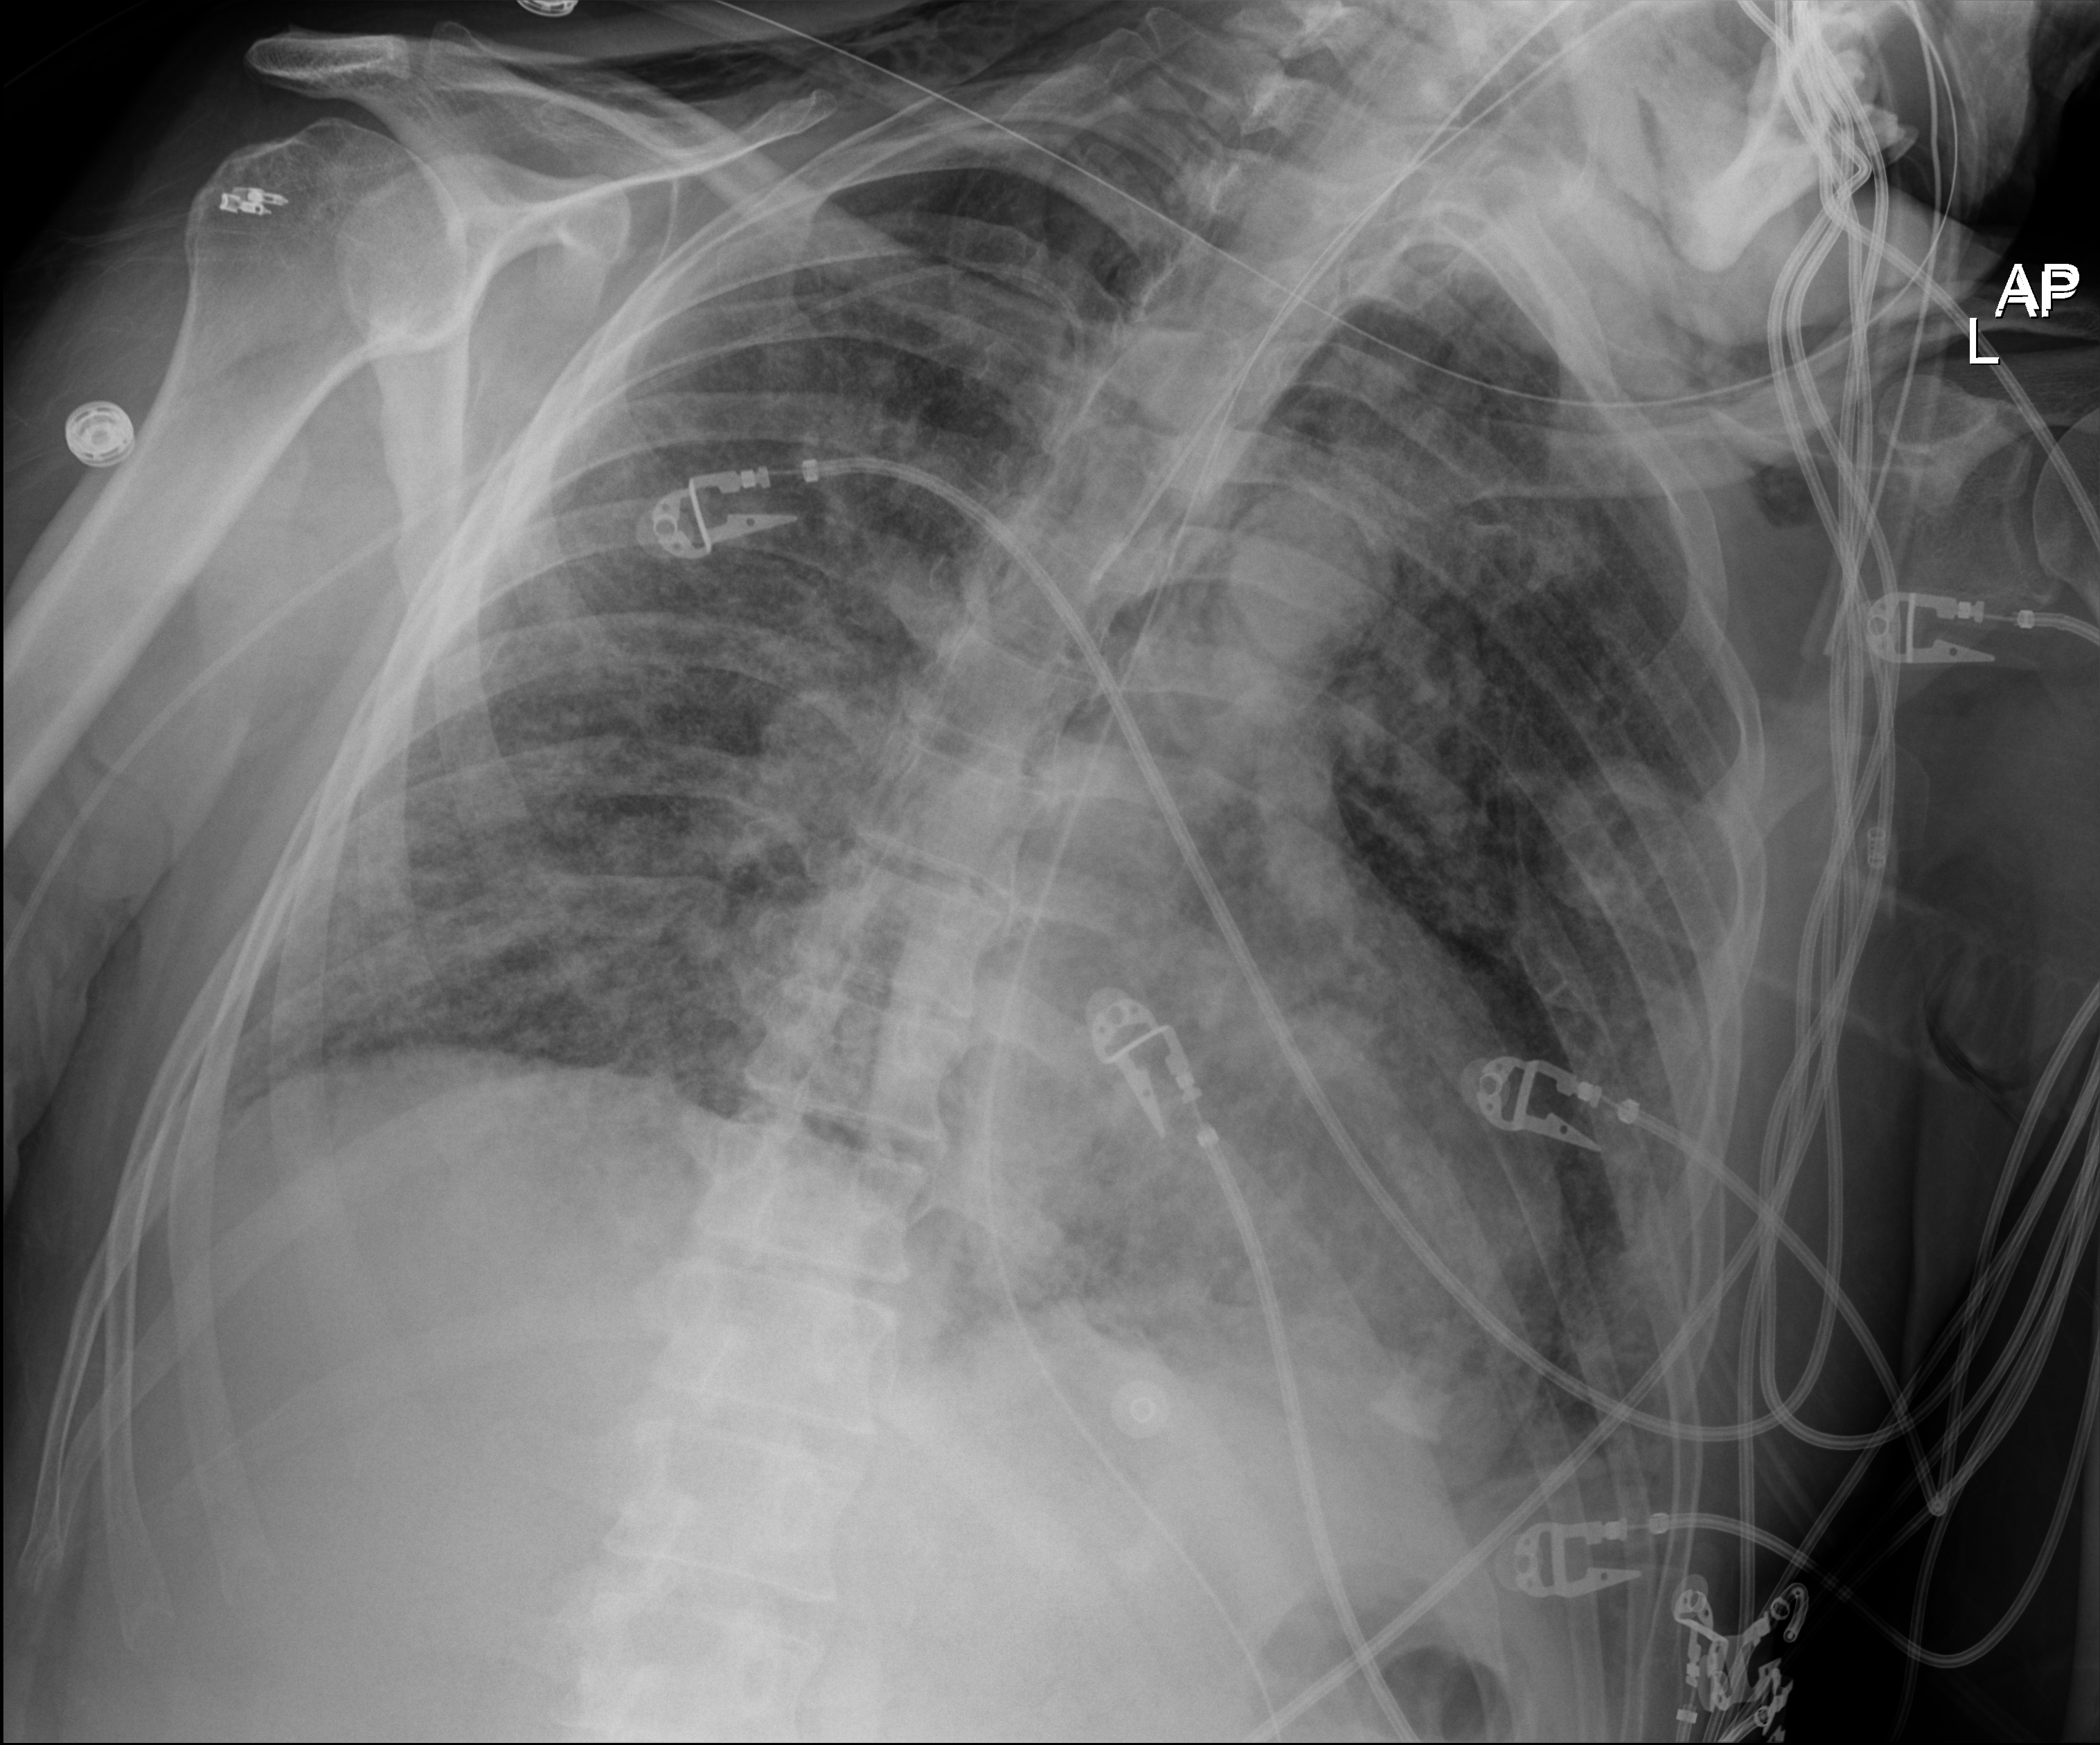
Chest X-ray (portable). Male patient hospitalised with COVID-19, age 60–74 years.
Admission-level facts for this patient (not findings on this image; timing relative to this image not recorded): admitted to intensive care during this hospital stay: yes; mechanically ventilated during this hospital stay: yes.